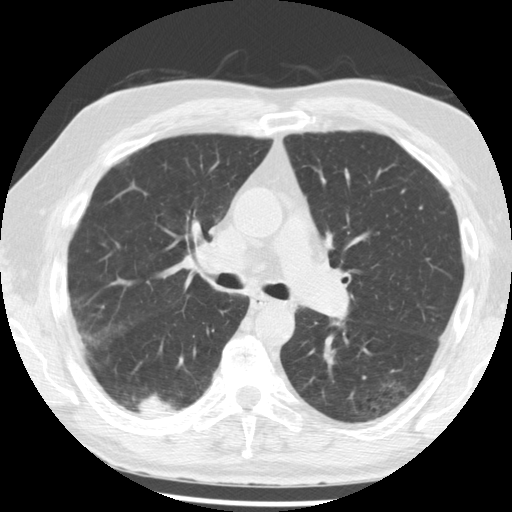
Low-dose screening chest CT, one axial slice; slice 126 of 221 in the series (ordered by position); reconstruction kernel STANDARD; 120 kVp; lung window (W 1500 / L -600 HU); 2.5 mm slice thickness; 512 × 512 image matrix, field of view 350 × 350 mm.
Structures marked on this image (outlined manually by an expert reader):
- lesion 1 (tumor, lower lobe of right lung): bounding box <138,395,185,417> (left, top, right, bottom; pixels)